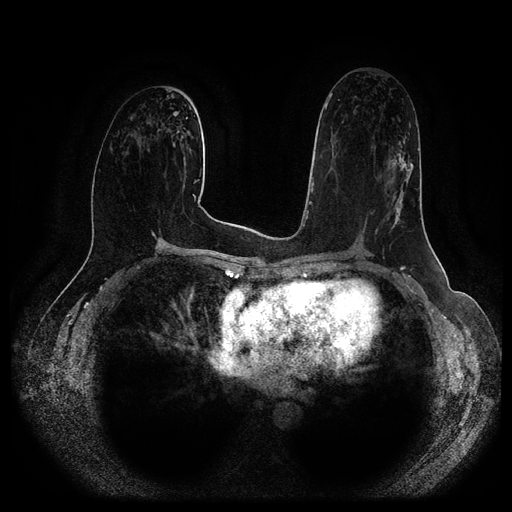
Breast MRI (dynamic contrast-enhanced, multi-phase), one axial slice; position 54 of 116 along the scan axis; dynamic contrast-enhanced series, time point 2 of 5 at this slice position (early post-contrast); 1.5 T; TE 2.6 ms, TR 5.2 ms; 512 × 512 image matrix, field of view 380 × 380 mm. Patient: female, 57 years.
Structures marked on this image (semi-automatically segmented with operator editing):
- breast lesion (labelled 'tumour' in the annotation; benign lesions carry a separate 'benign' label): bounding box [x1, y1, x2, y2] px = [387, 133, 413, 230]